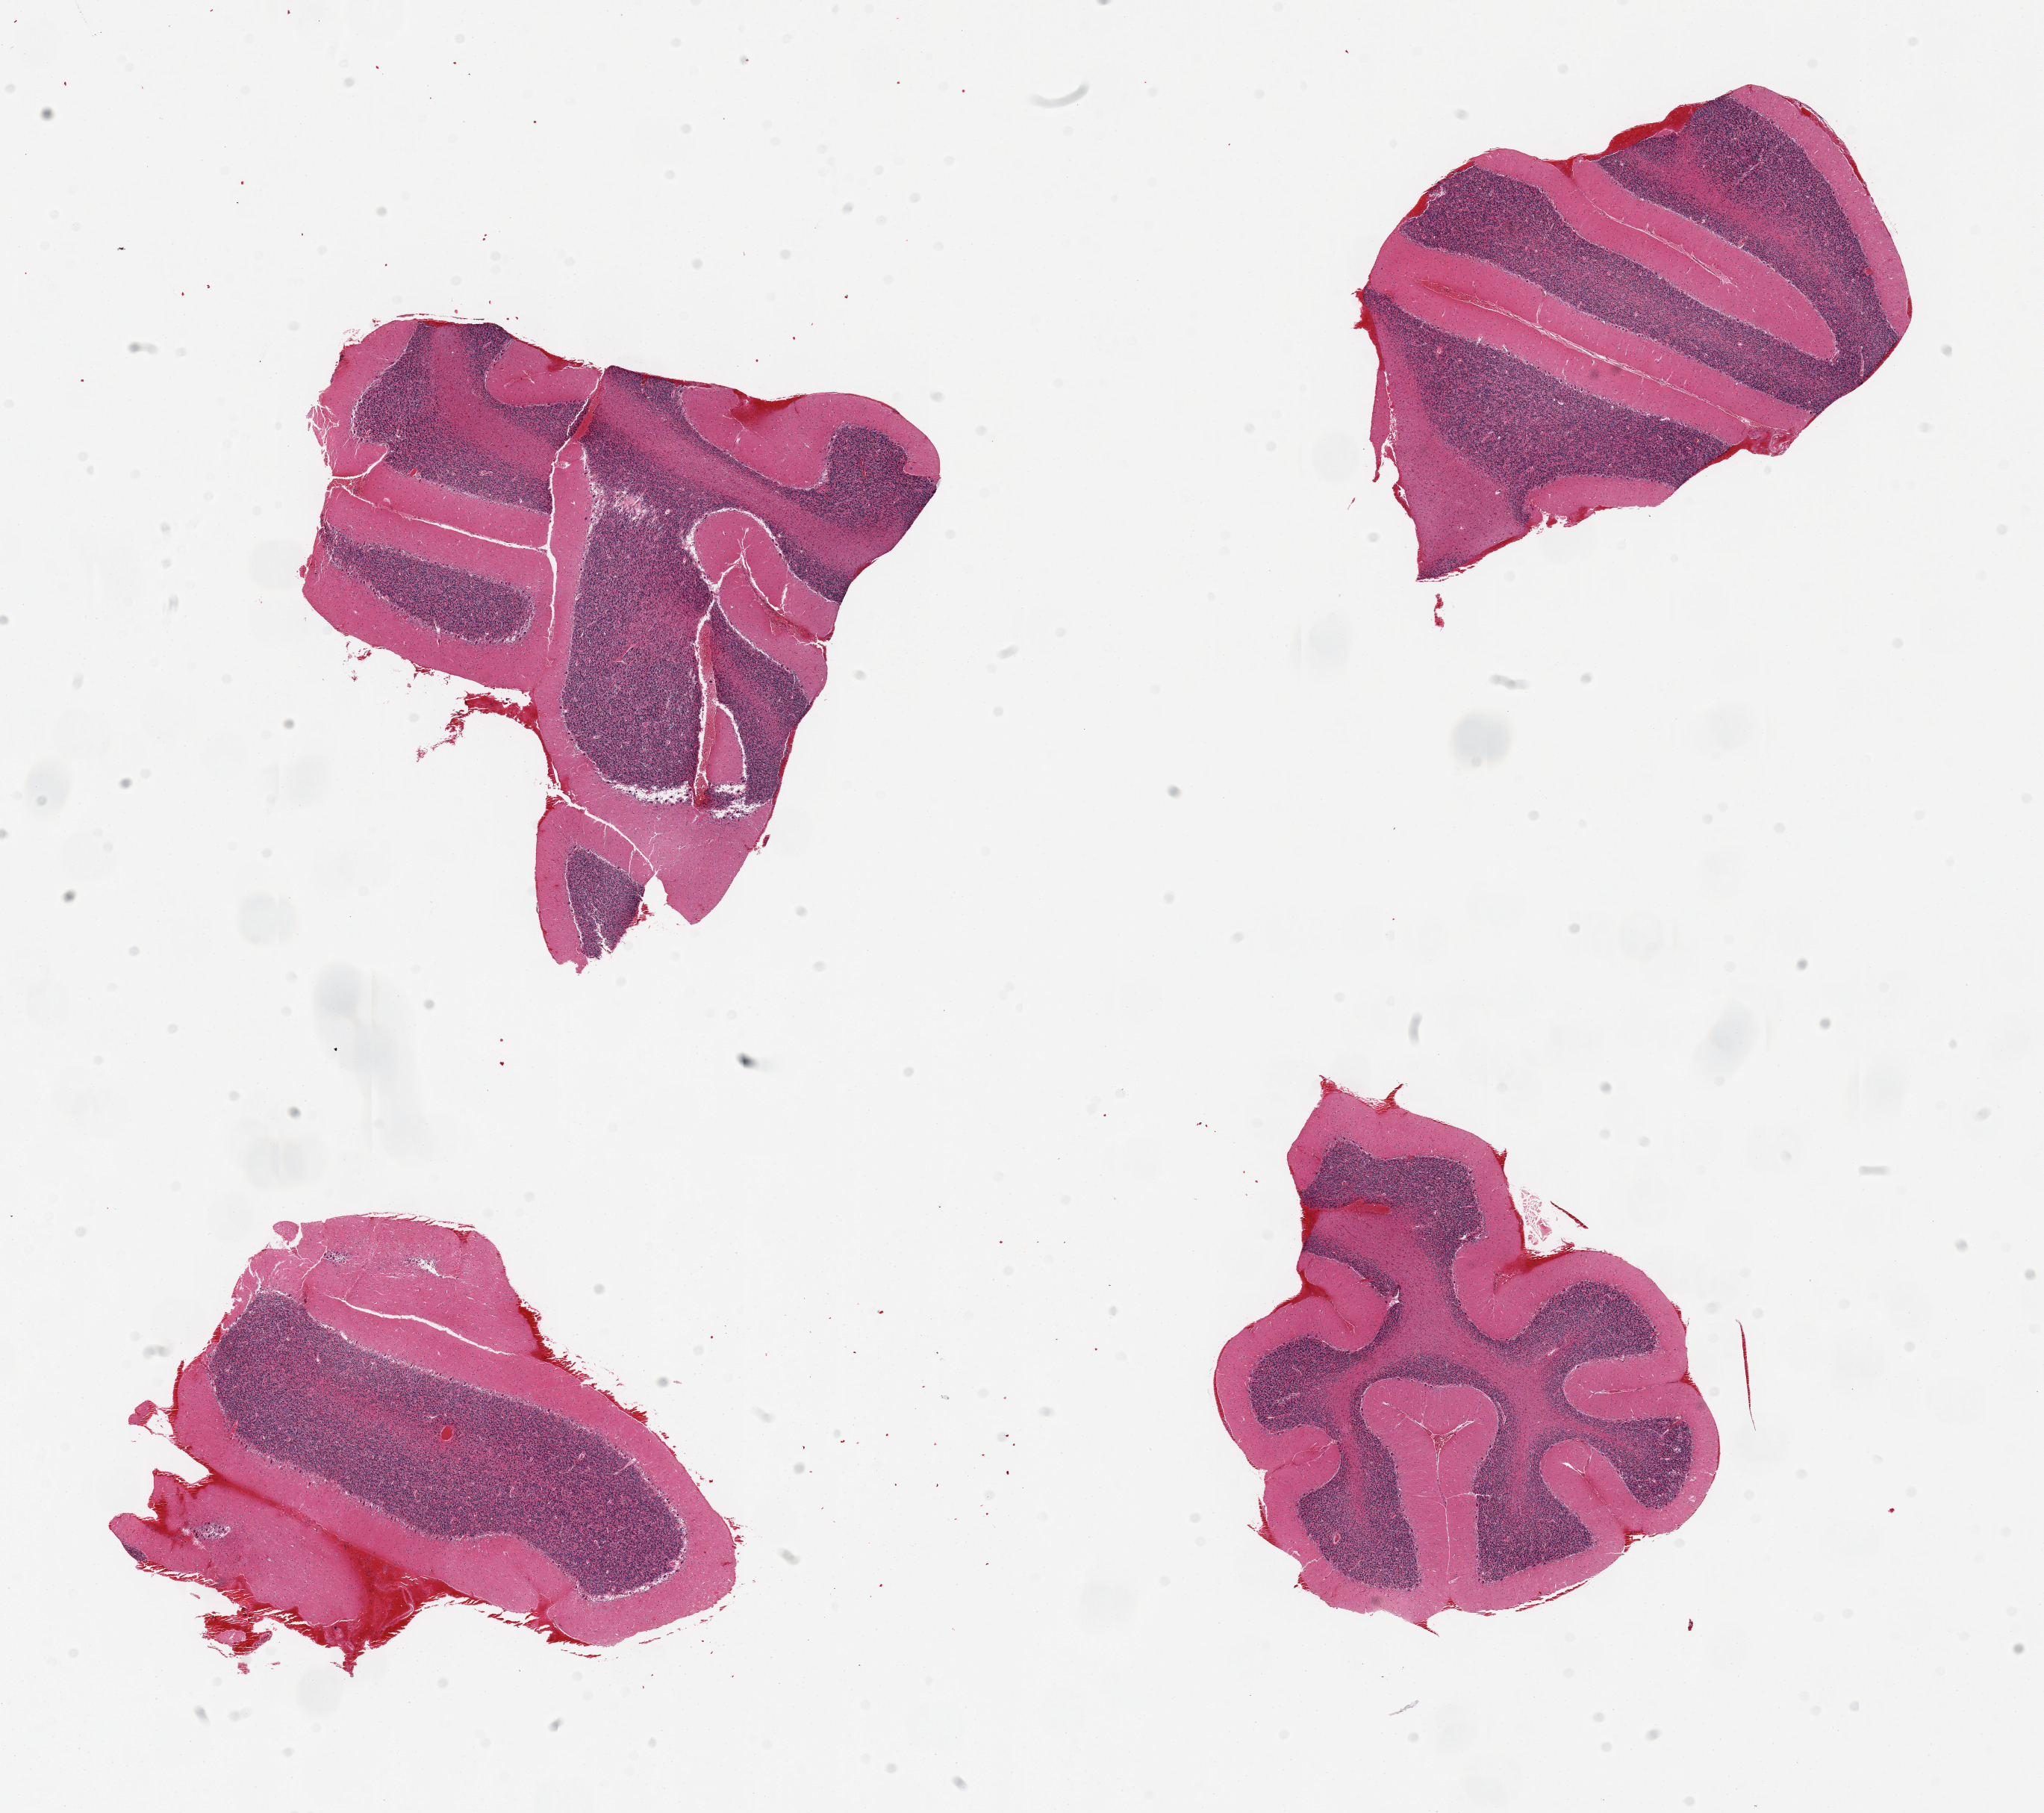
Digitized H&E-stained section, shown as a low-resolution overview of the whole scanned area (about 21.7 x 19.2 mm); PAXgene-fixed, paraffin-embedded tissue; target tissue: cerebellum; donor tissue sample.
Review note (as recorded): 4 pieces; prominent subarachnoid hemorrhage with focal parenchymal dissection.